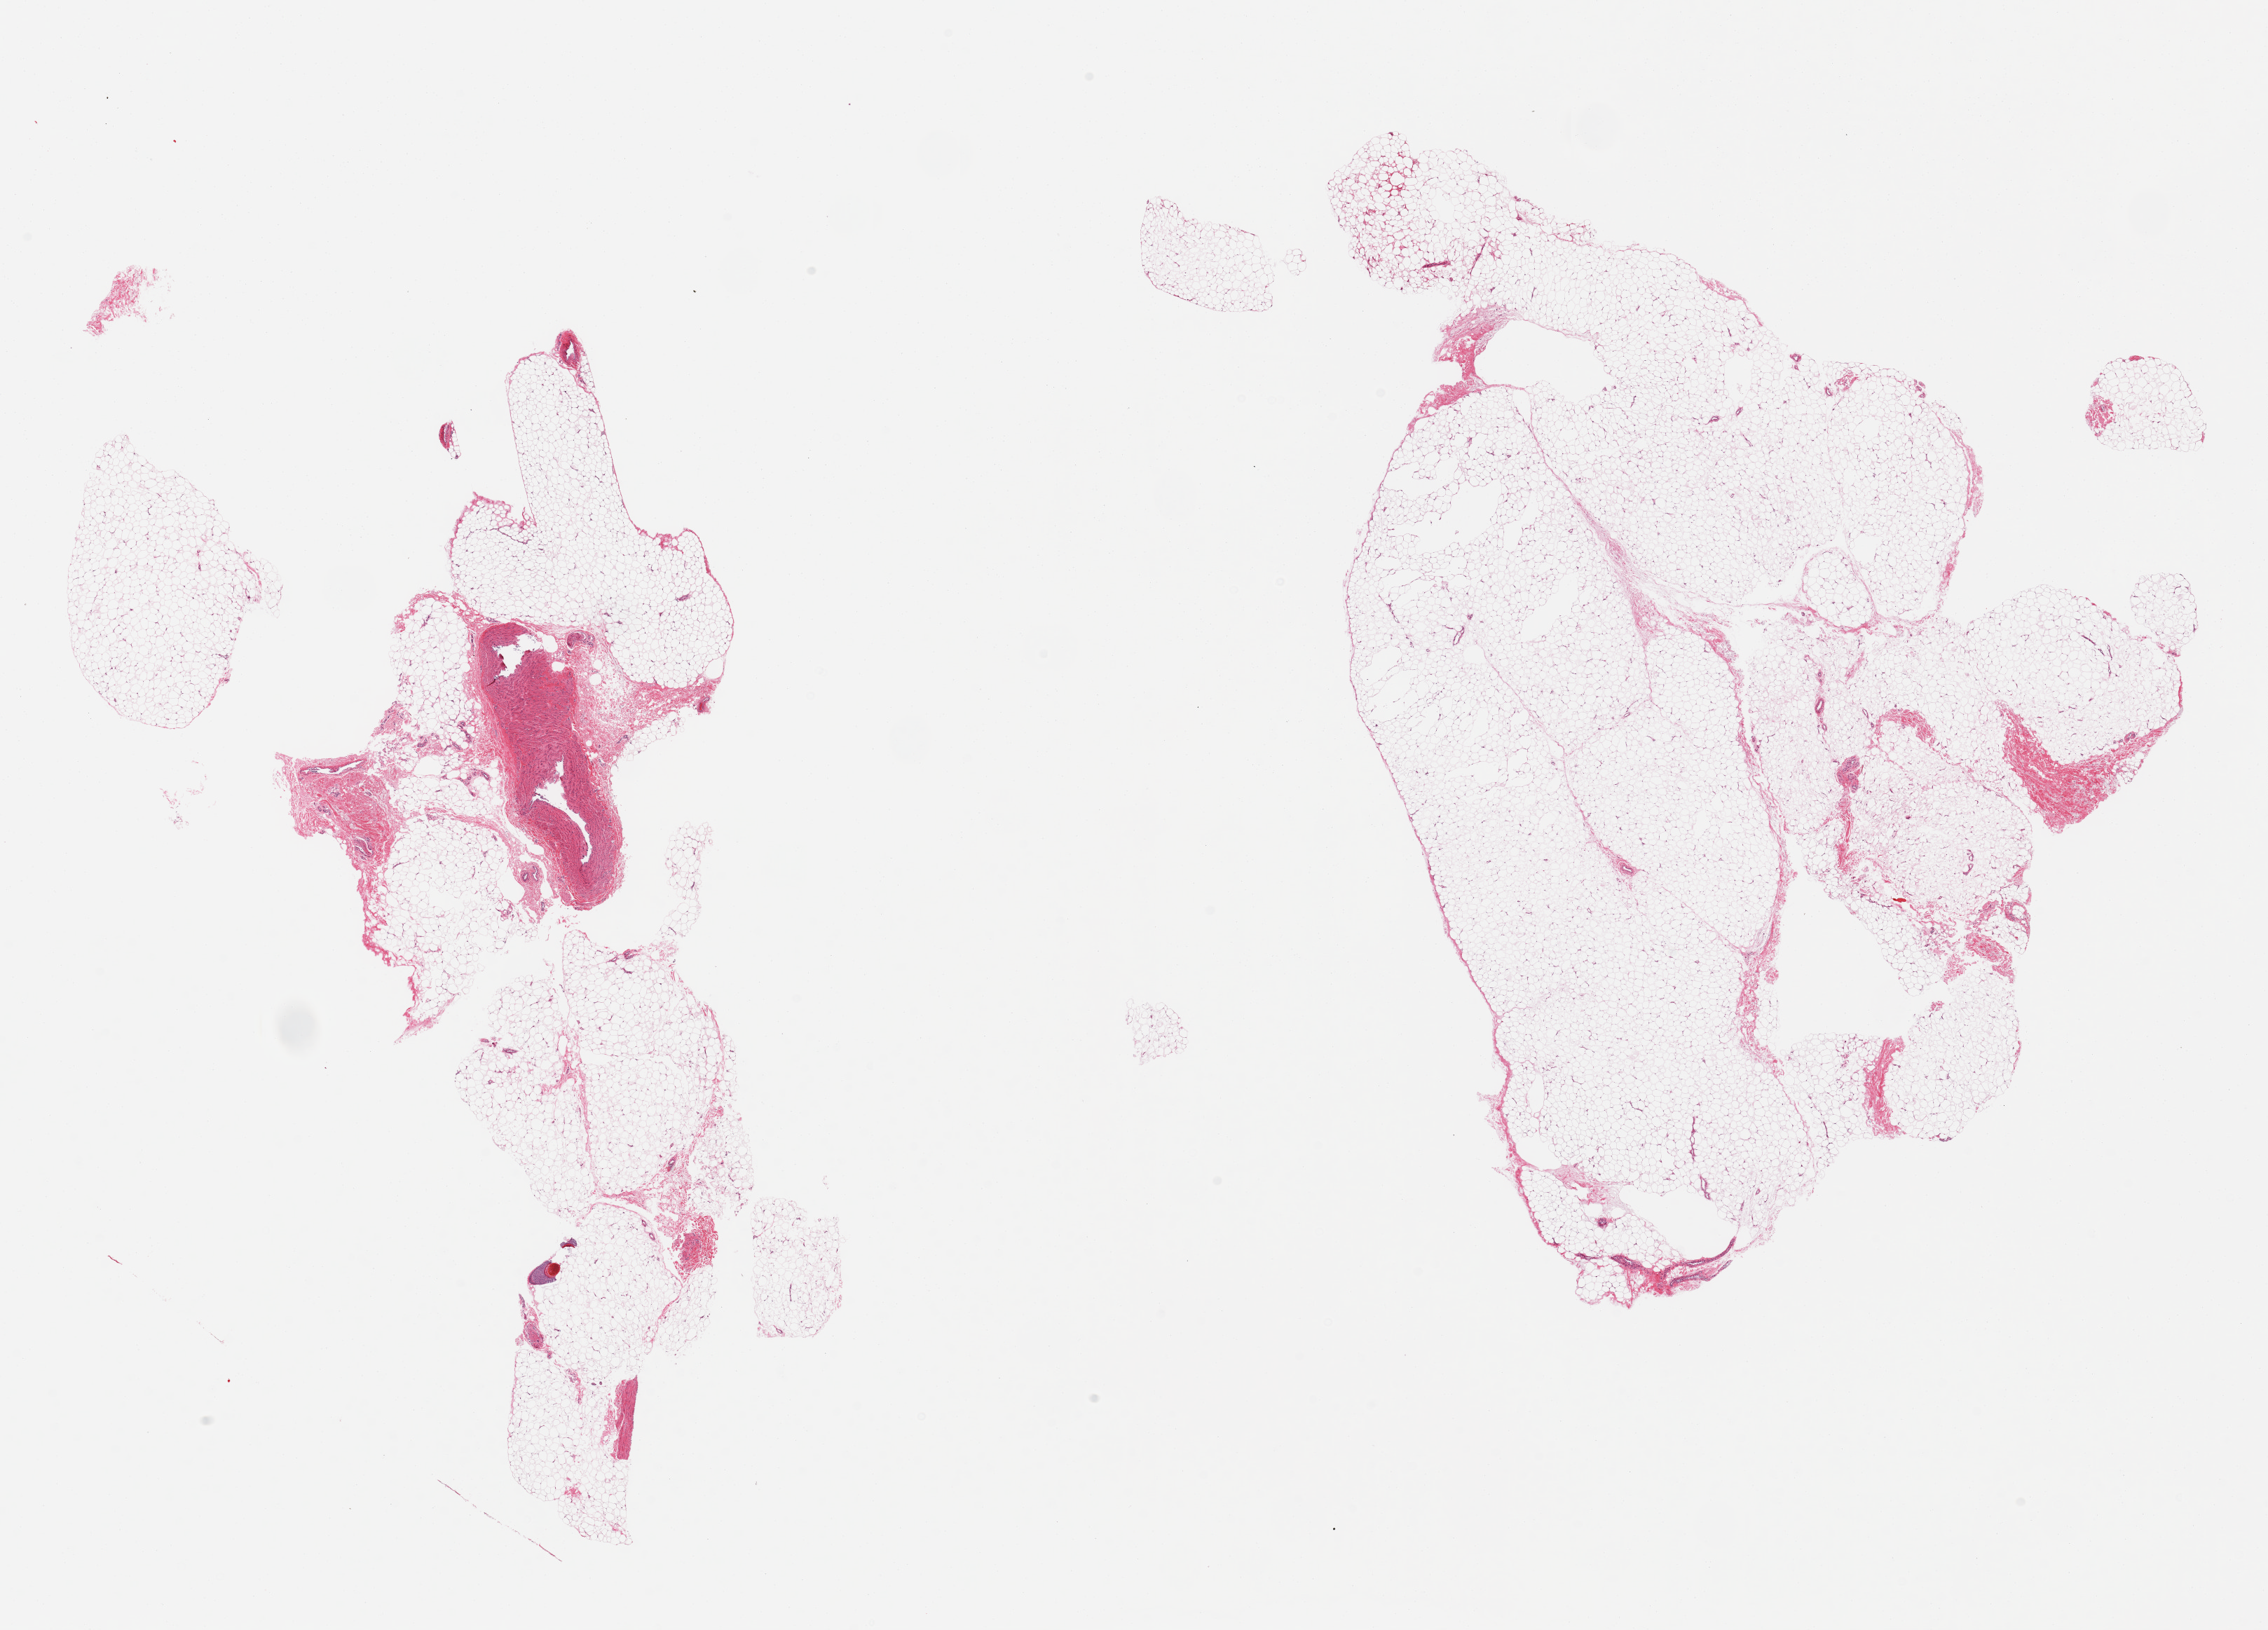
Hematoxylin and eosin (H&E) whole-slide image, brightfield — shown as a low-resolution overview of the whole scanned area (about 25.6 x 18.4 mm). PAXgene-fixed paraffin-embedded (PFPE) section. Target tissue: adipose tissue. Tissue donor sample. Donor sex: male.
Reviewer comment on this tissue sample: 2 pieces, ~10% vascular/connective tissue.